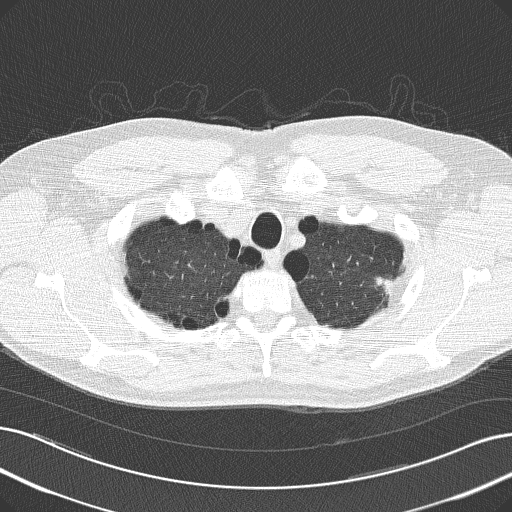
Low-dose screening chest CT, axial slice. First (baseline) screen. Lung window (W 1500 / L -600 HU). 512 × 512 image matrix, field of view 366 × 366 mm. Male participant, aged 62 years at enrolment.
Expert reader's lesion annotation, bounding box [x1, y1, x2, y2] px = [350, 255, 406, 311]. The screening reader recorded 4 non-calcified nodules or masses ≥4 mm on this exam (left upper lobe, right upper lobe, right upper lobe, right middle lobe); which of them this box marks is not recorded.